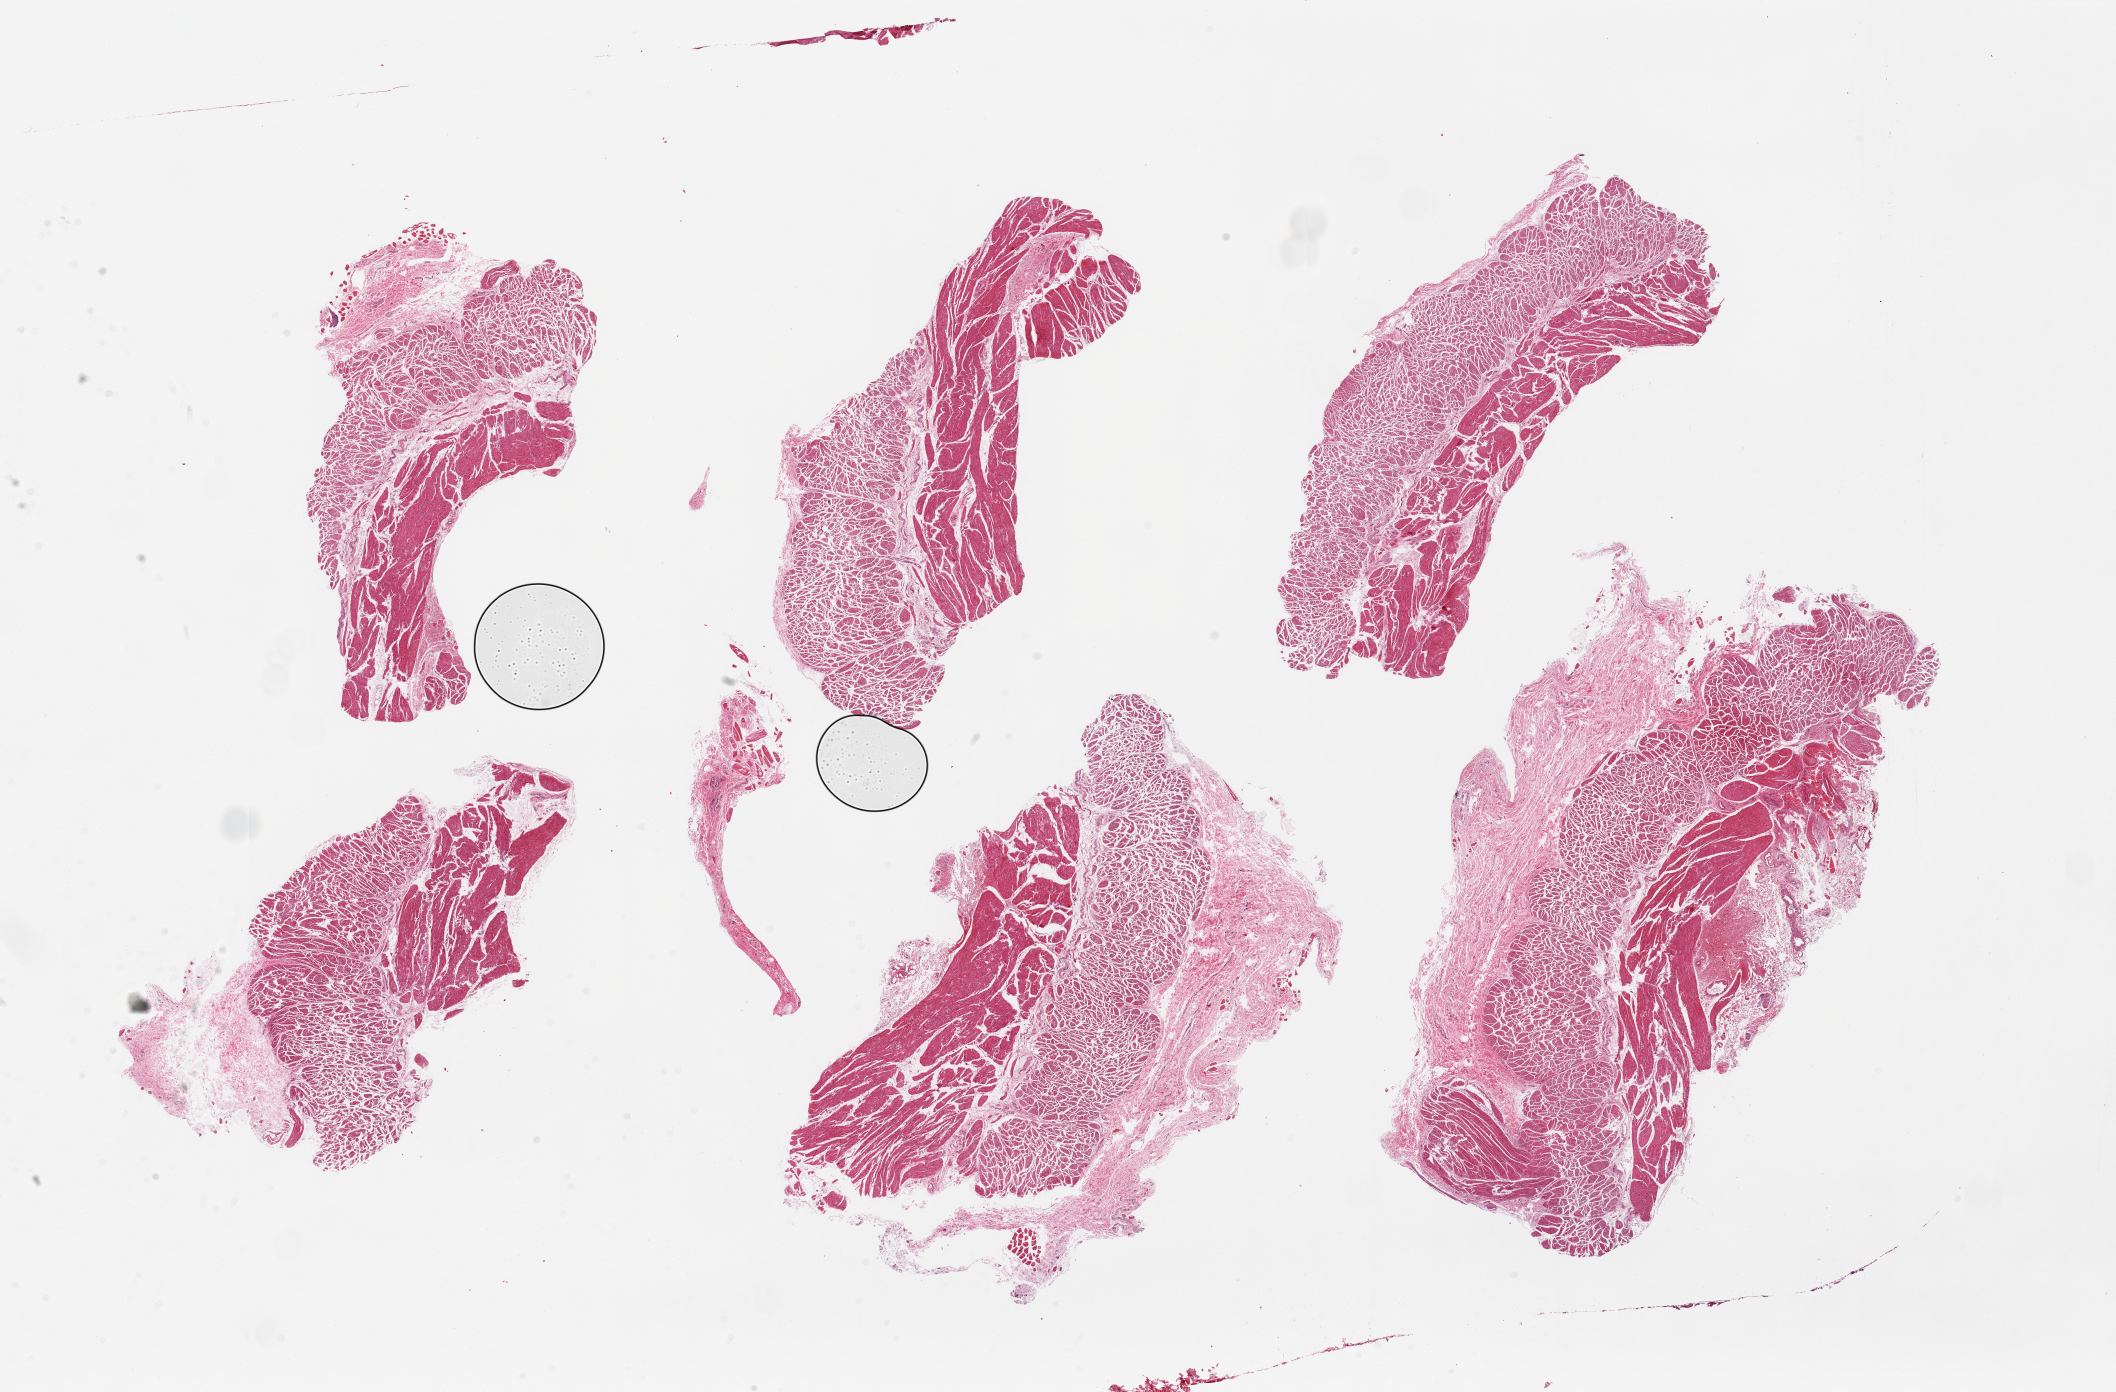
Hematoxylin and eosin (H&E) whole-slide image, shown as a low-resolution overview of the whole scanned area (about 33.5 x 22.0 mm, slide scanned at 20x); PAXgene-fixed, paraffin-embedded tissue; sampled site (target tissue): esophageal muscle; donor tissue sample. Donor: female.
Review note (as recorded): 6 pieces. up to 11.5x7mm; Up to 2mm of periesophageal extraneous fibrous stroma.